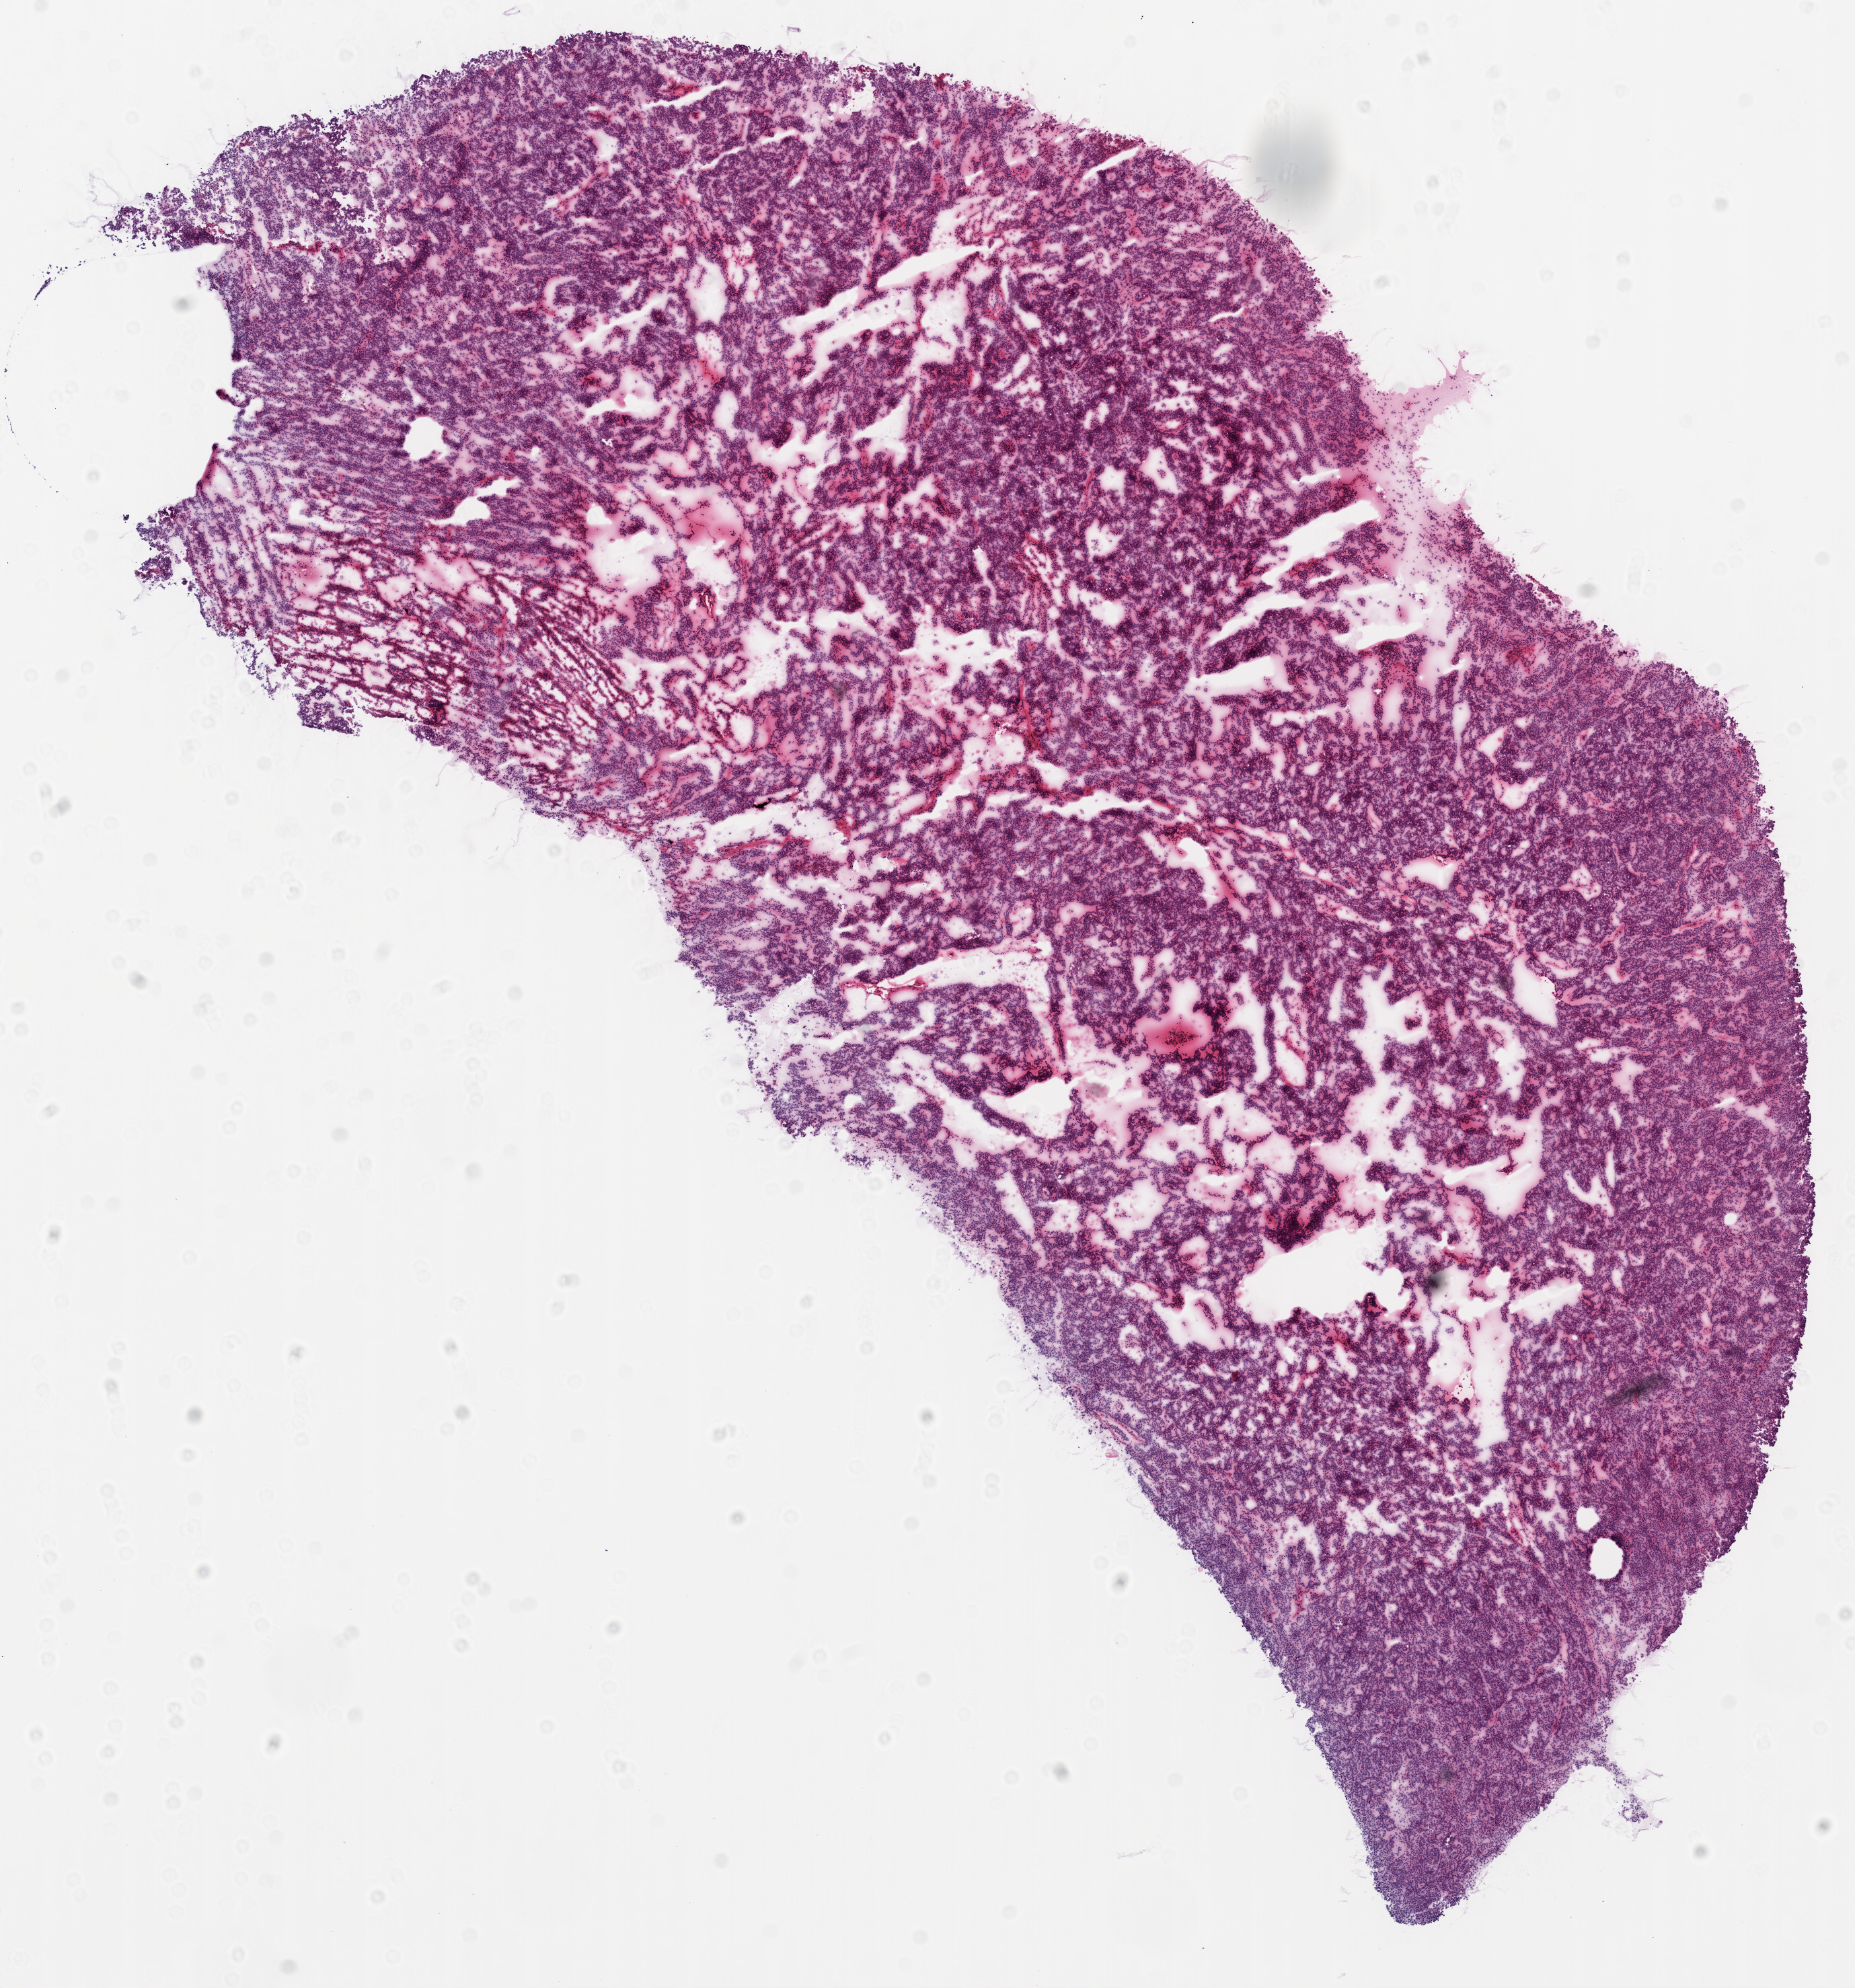
H&E-stained whole-slide image, a low-resolution overview of the entire scanned area, about 11.1 x 11.9 mm; frozen section; sample: primary tumour, ovary. Female patient; age at initial diagnosis 50 years. Histologic grade: G3 (poorly differentiated). Pathologist review of this section (percent, as recorded): tumour cells 95%, tumour nuclei 90%, normal cells 0%, stromal cells 5%, necrosis 0%.
Histologic diagnosis: Serous cystadenocarcinoma, NOS. FIGO stage: IIIC. Laterality: bilateral.